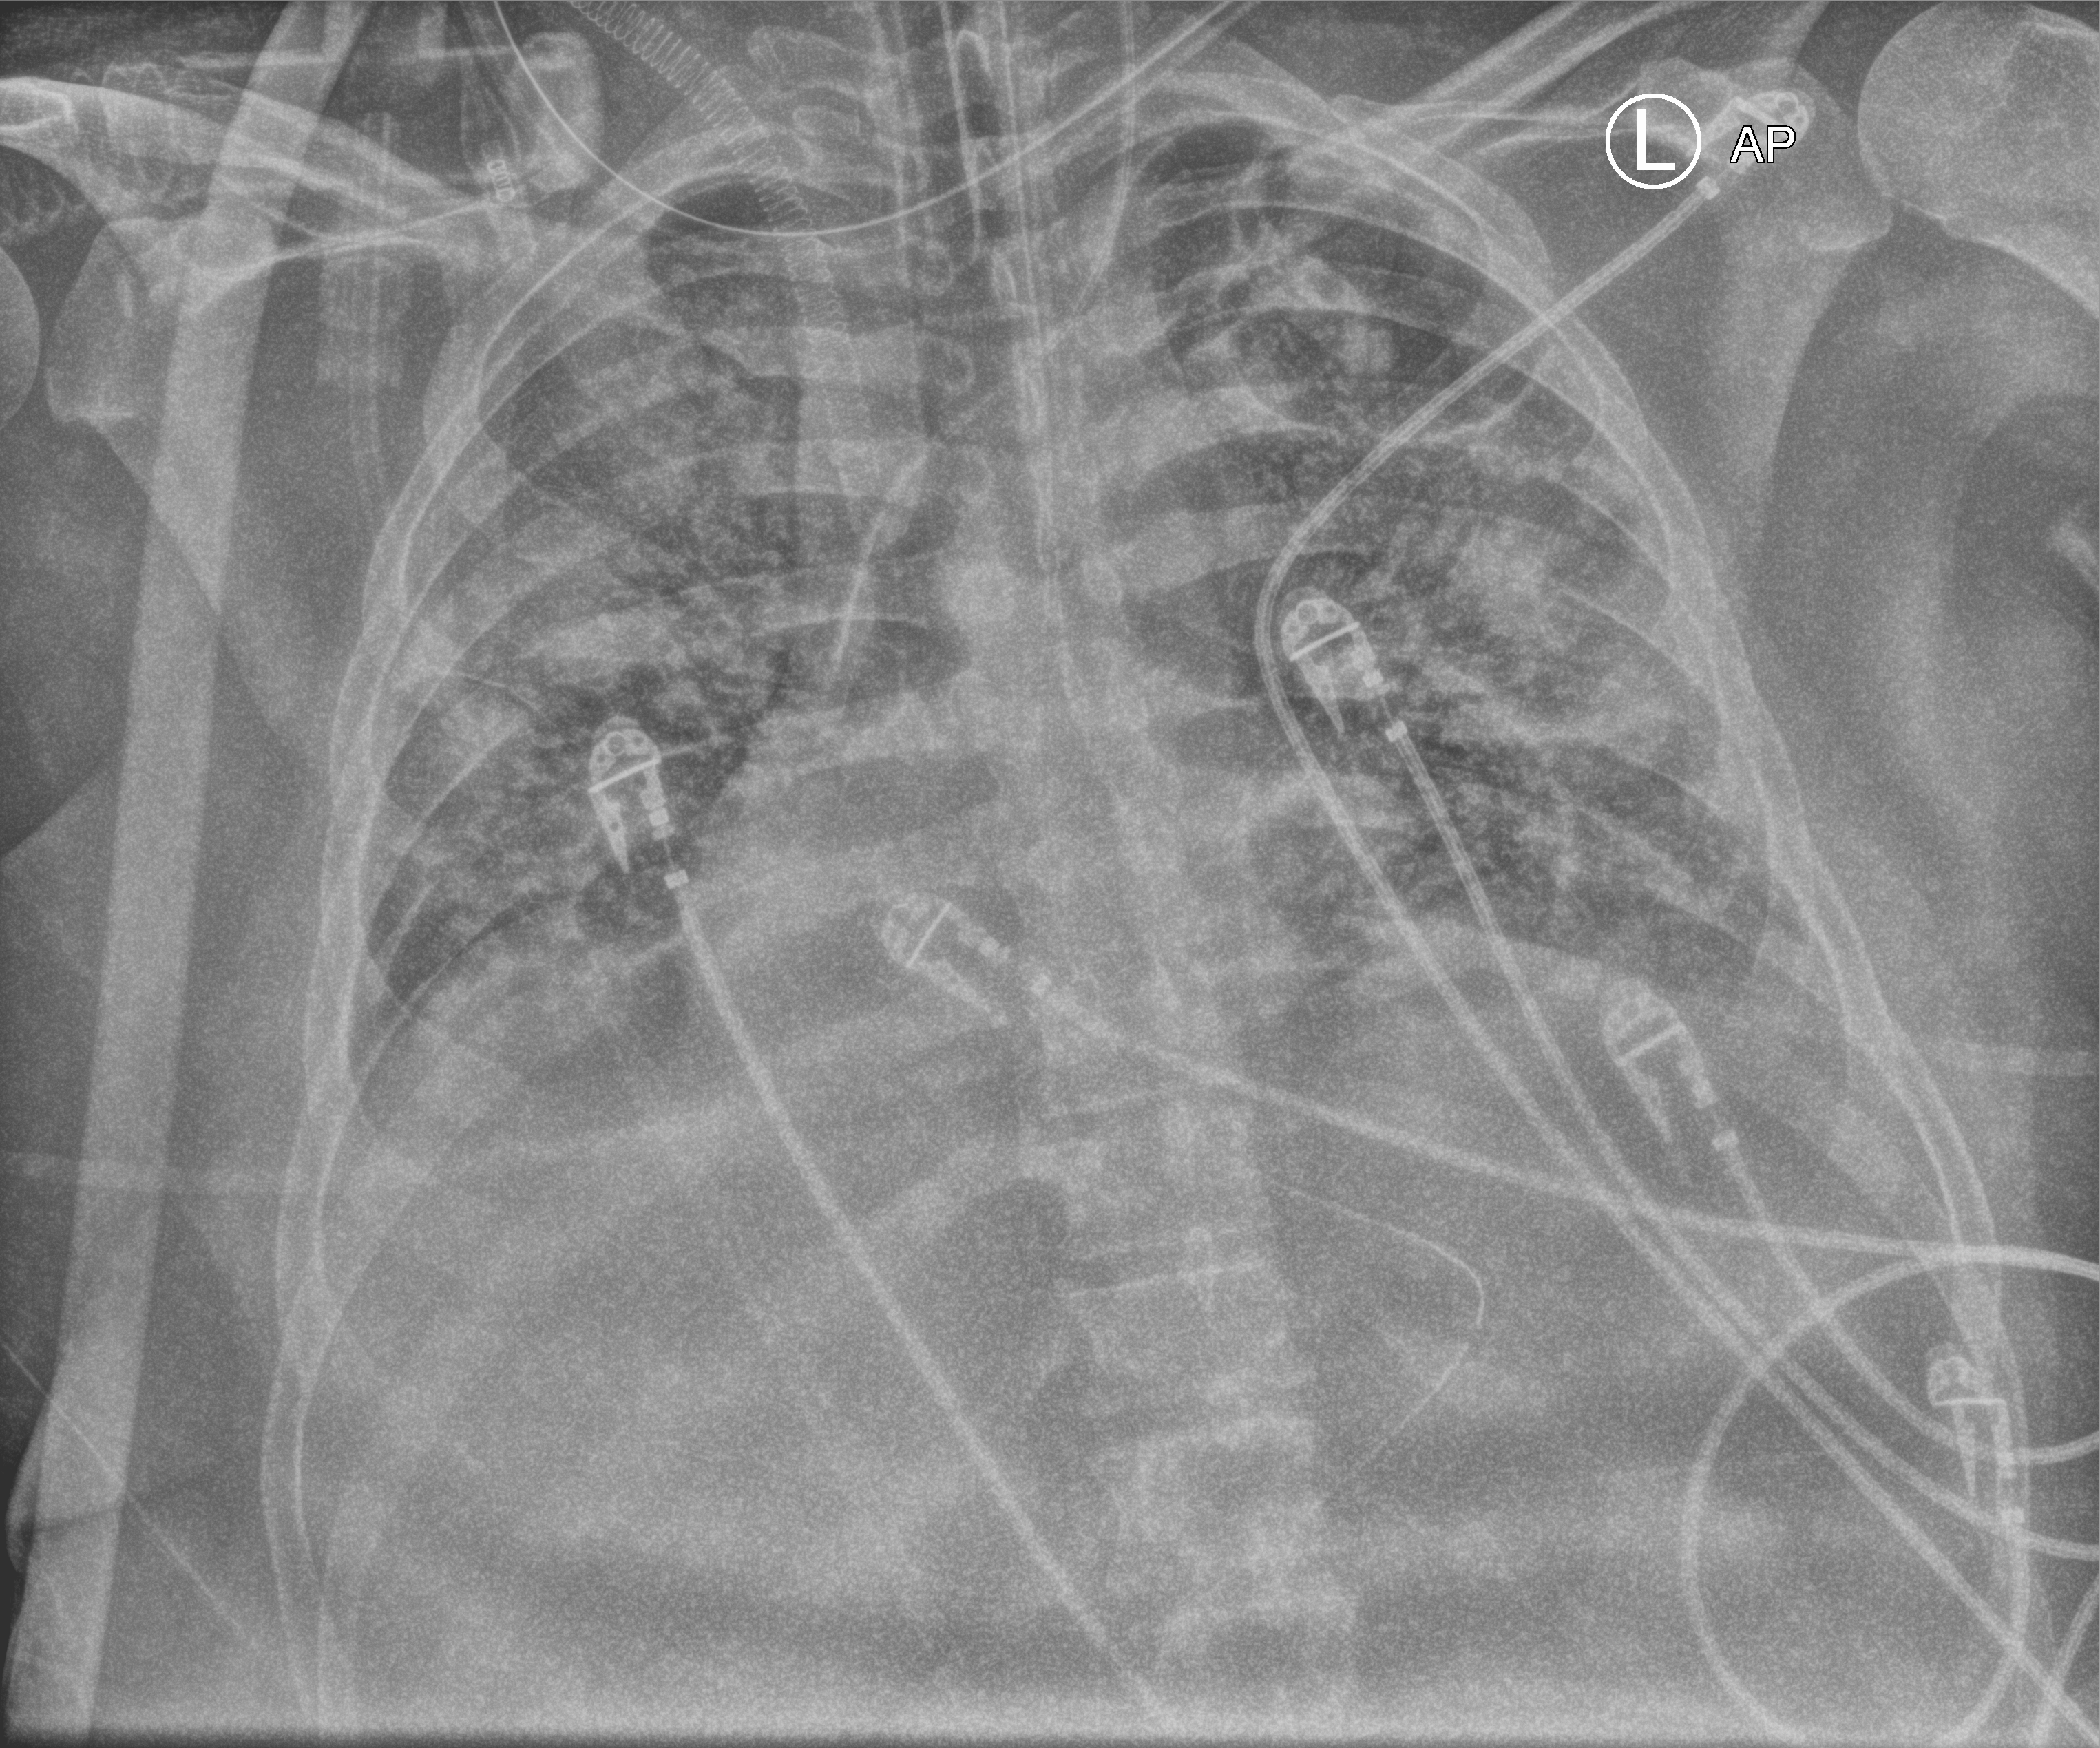
Portable chest radiograph, anteroposterior (AP) projection. Patient hospitalised with COVID-19, aged 18–59 years.
From the hospital-stay record, not from the radiograph (when in the stay this image was taken is not recorded): mechanically ventilated during this hospital stay: yes; admitted to intensive care during this hospital stay: yes.